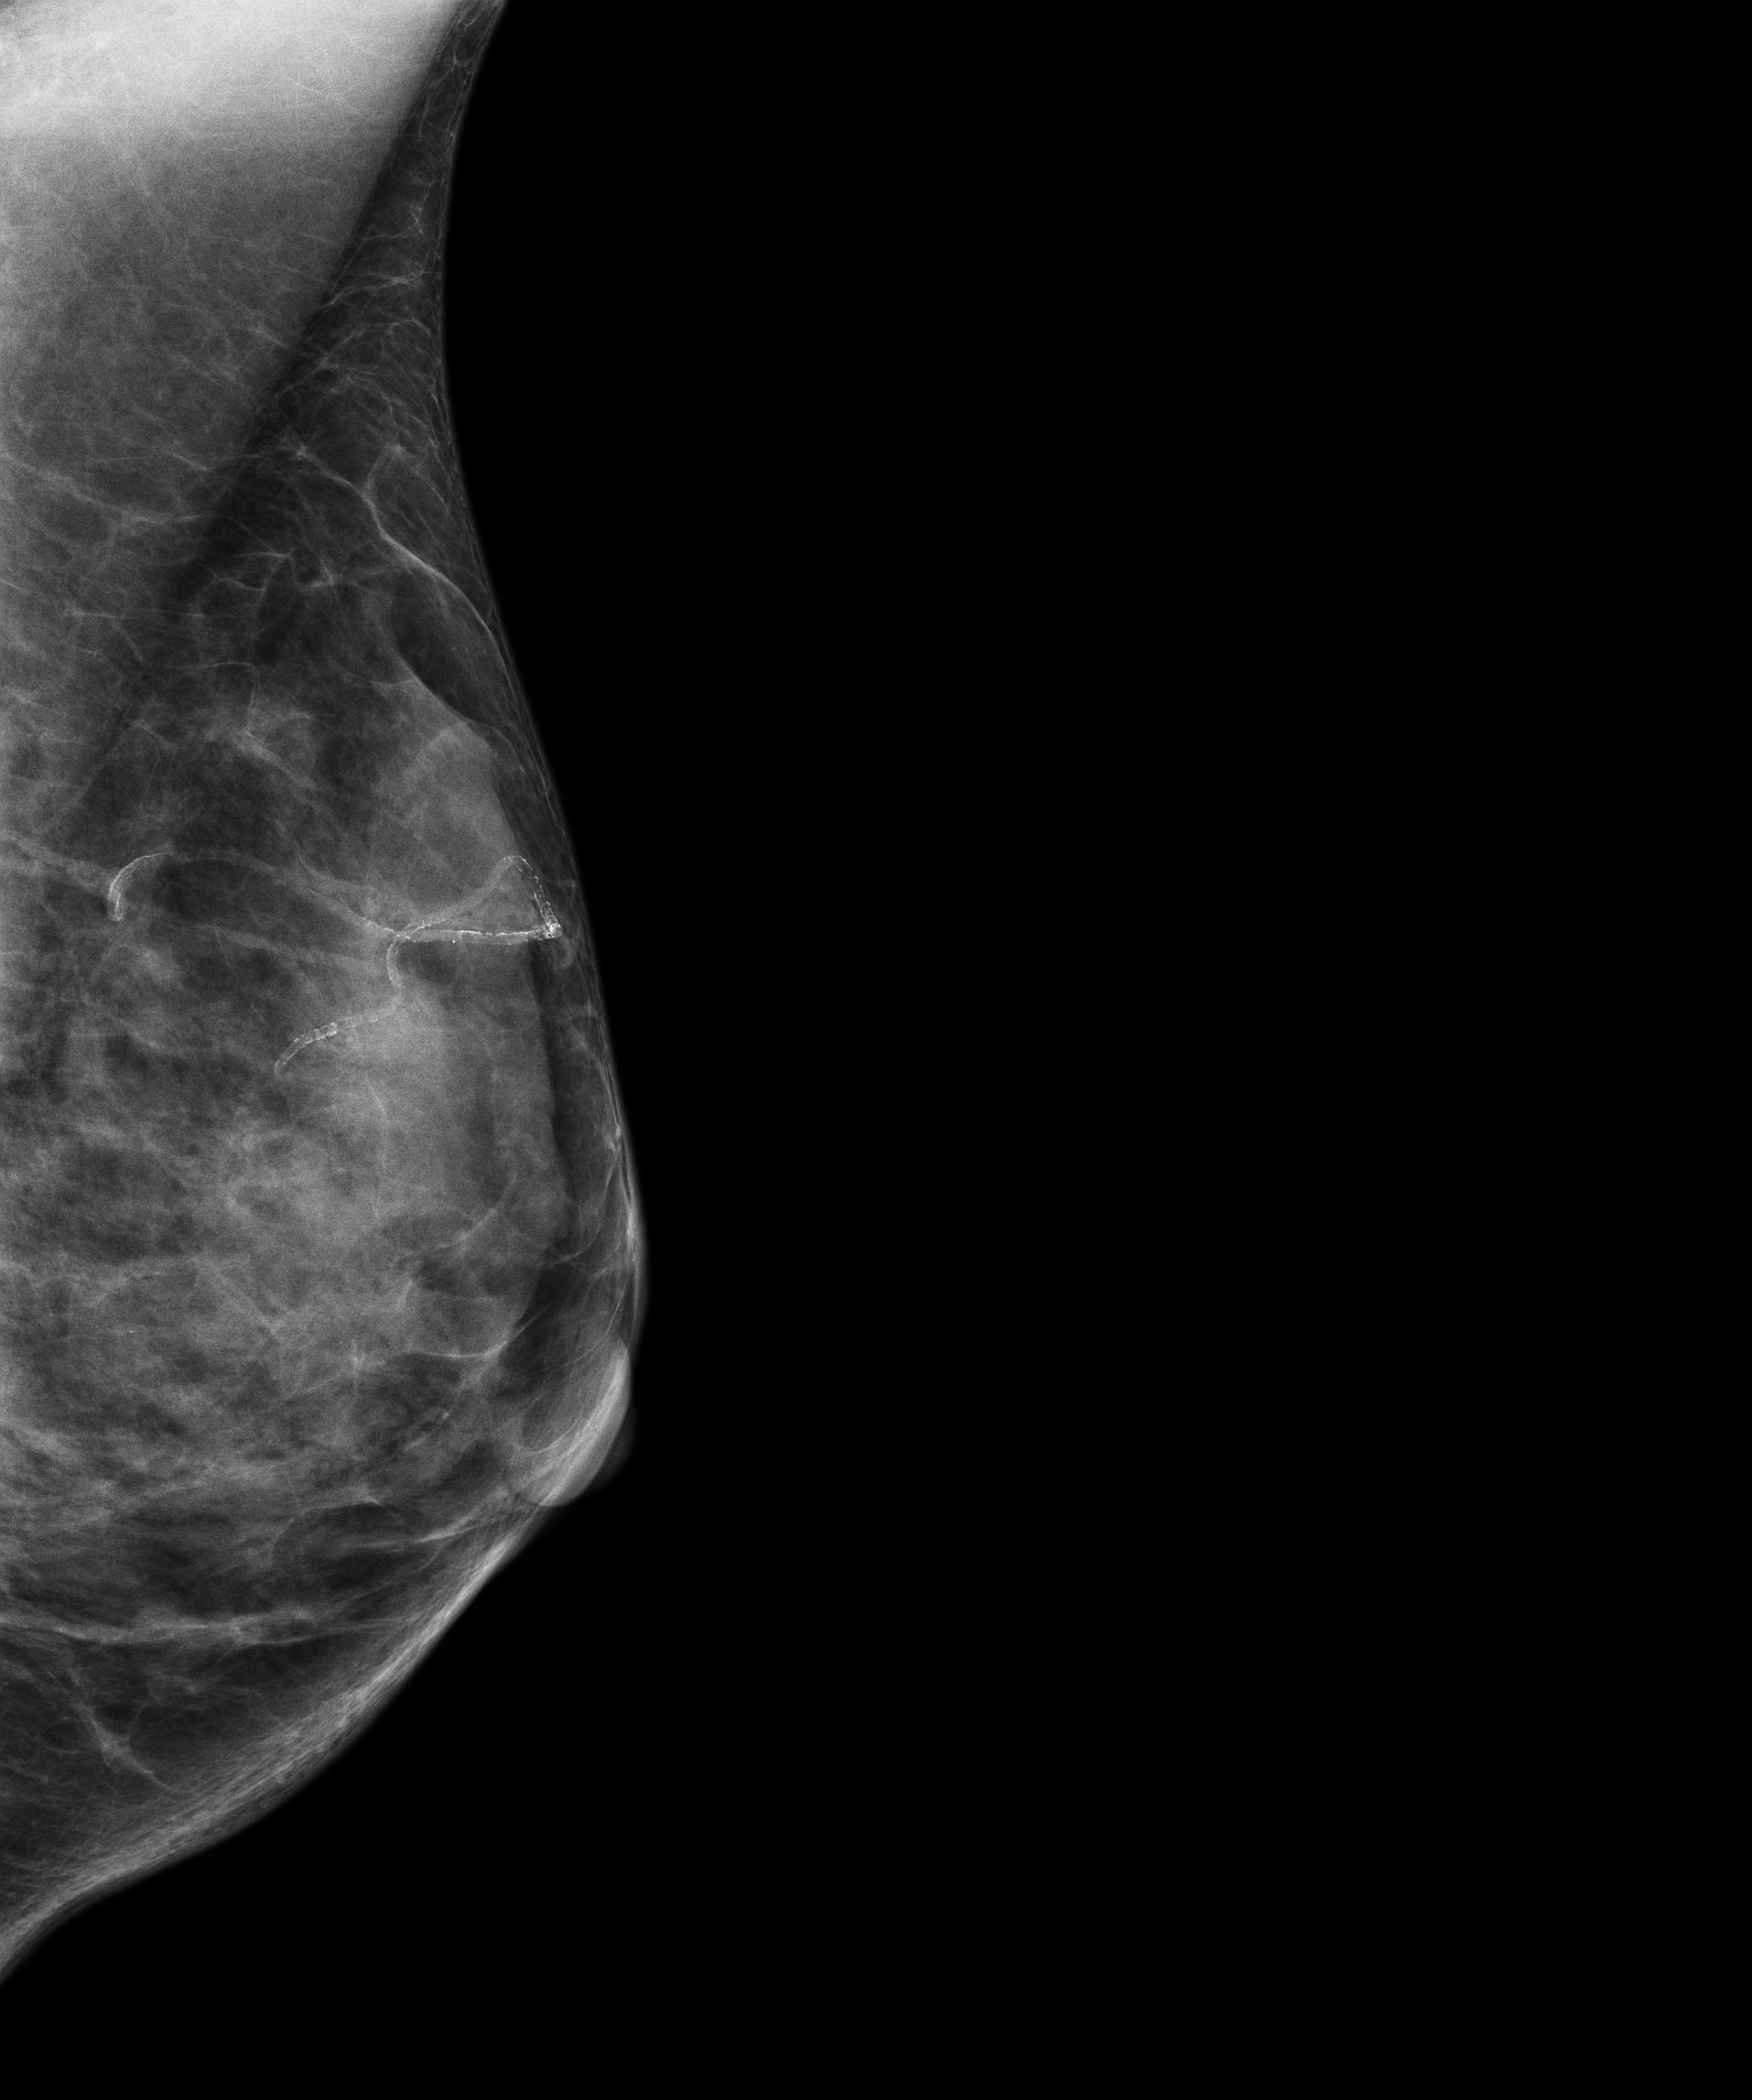
Digital mammogram (FFDM); left breast; medio-lateral oblique projection; screening examination. Female patient, age 59 years.
BI-RADS breast density category at the screening exam (both breasts, scale 1–4): 4. Final BI-RADS category for the screening round (tomosynthesis exam, both breasts): category 1. Recall: no recall after this screen.